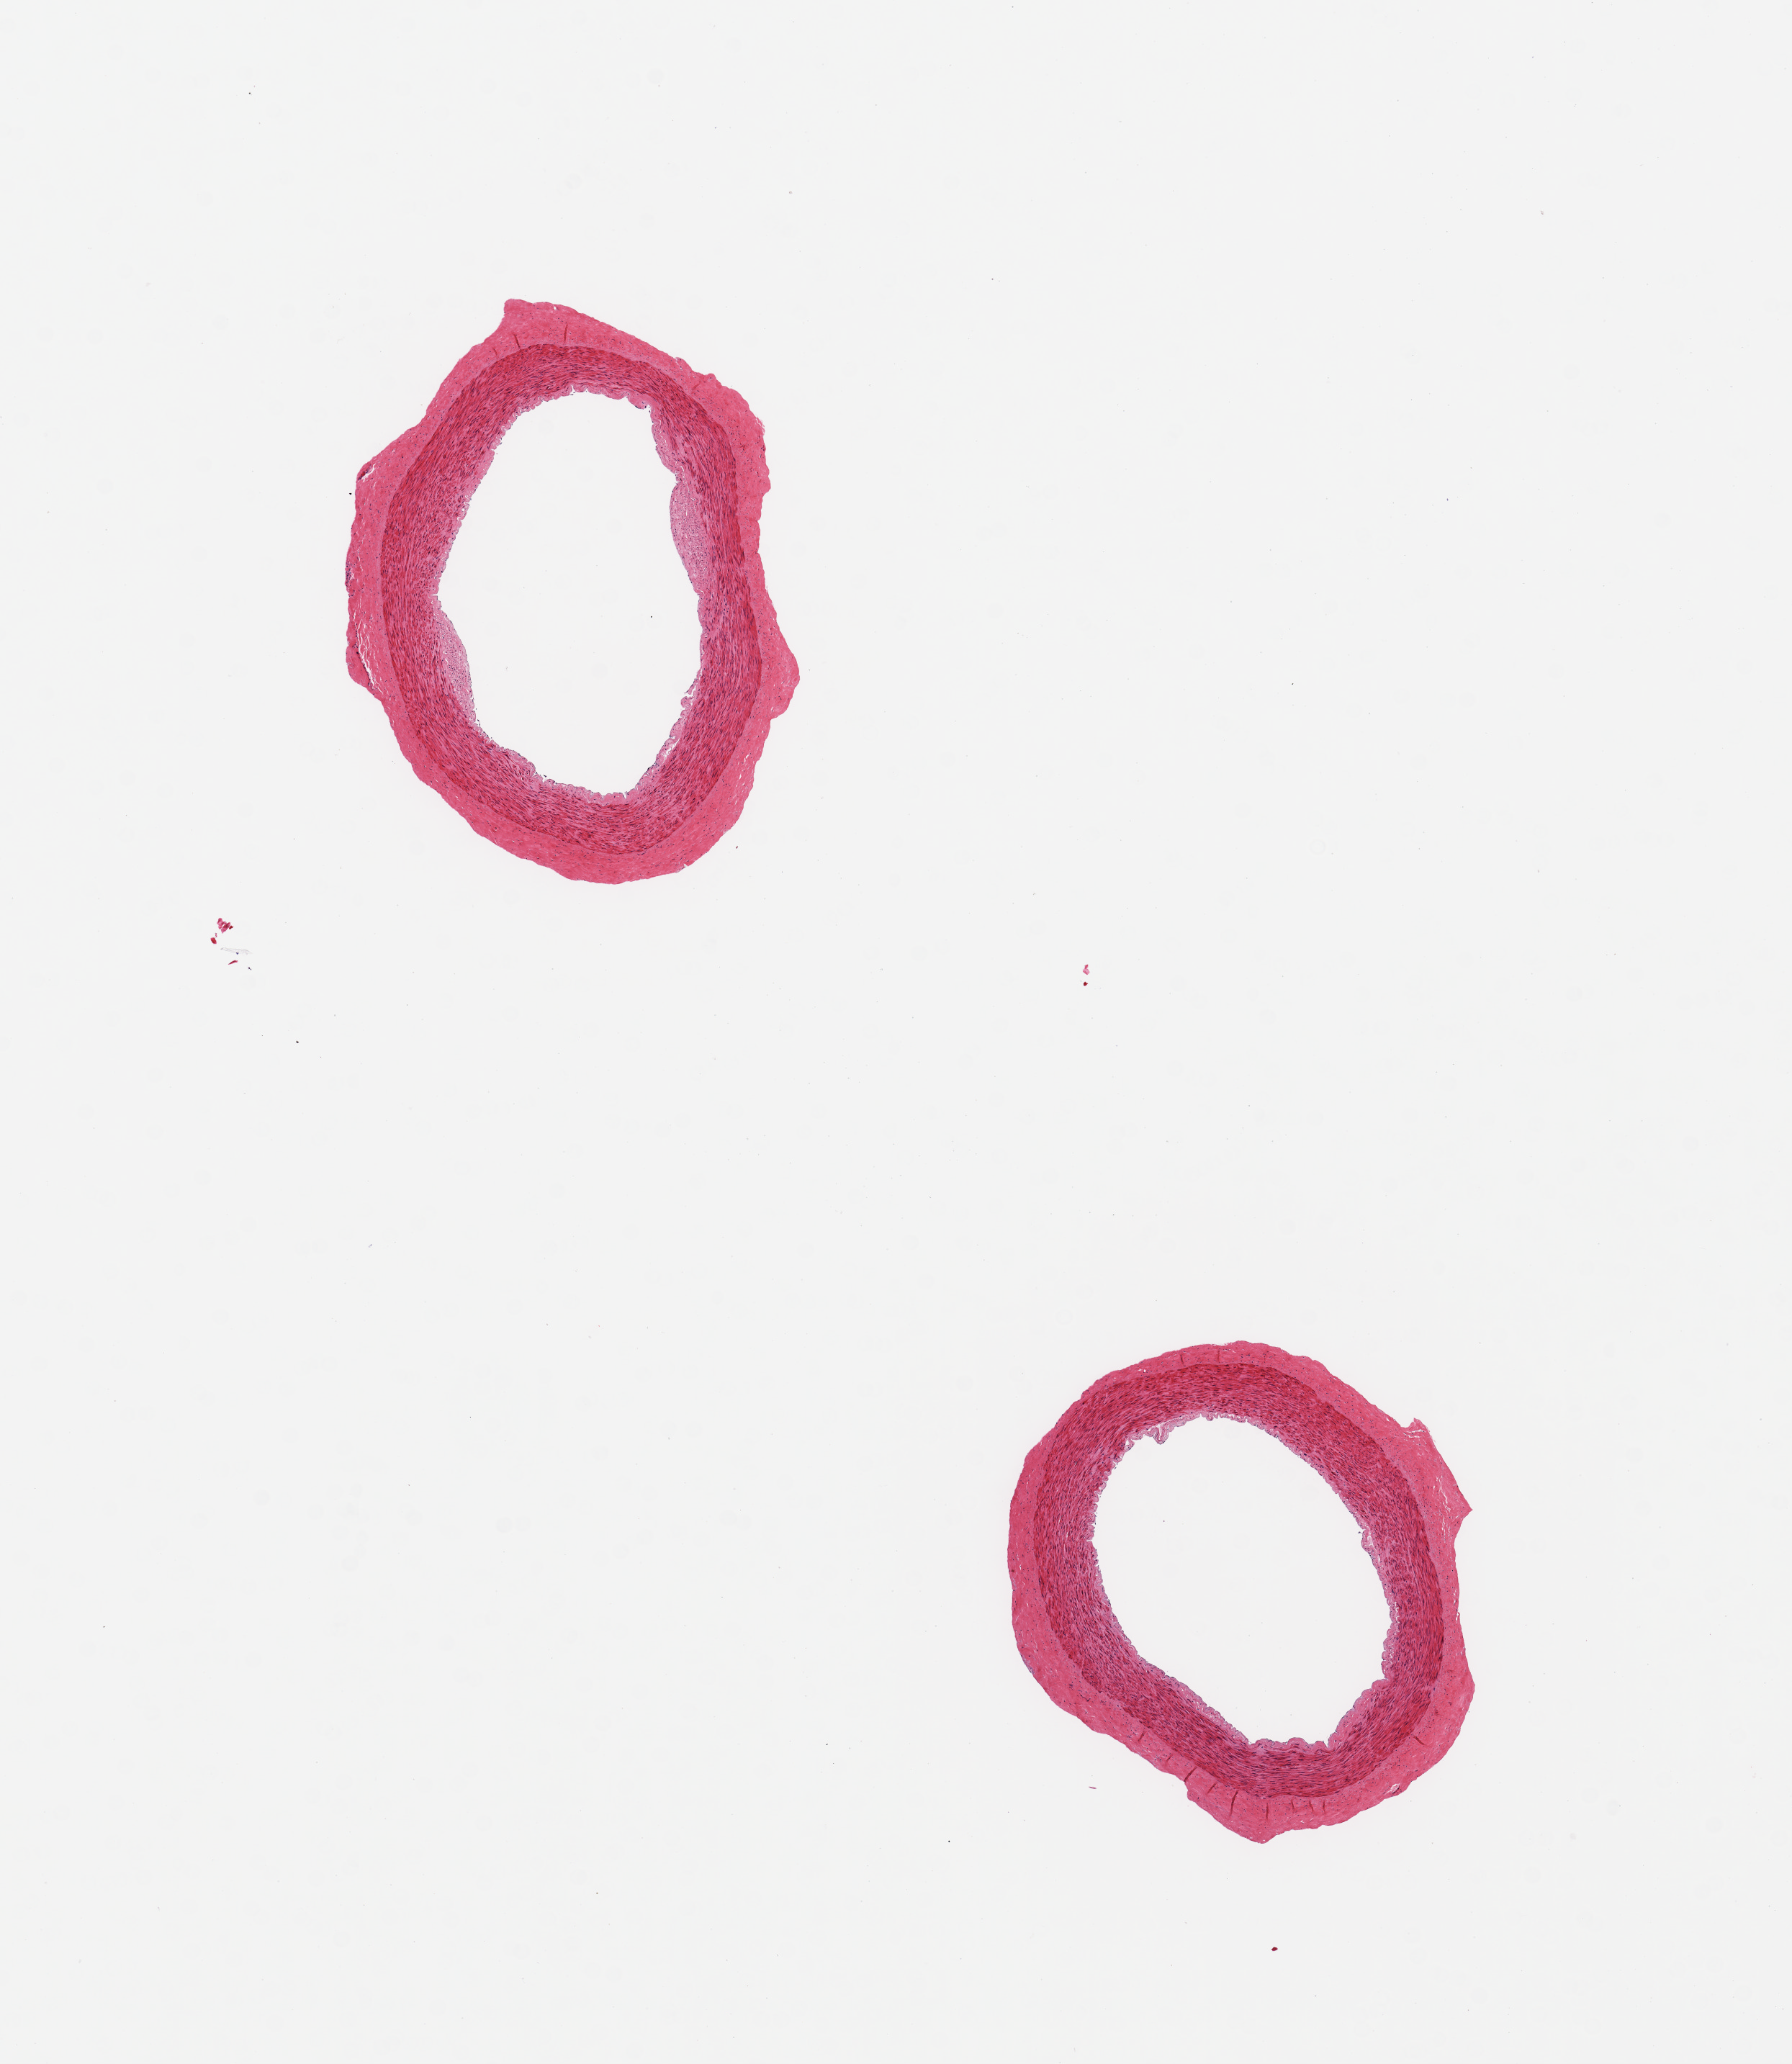
Hematoxylin and eosin (H&E) whole-slide image, shown as a low-resolution overview of the whole scanned area (about 9.8 x 11.3 mm, from a 20x scan), PAXgene-fixed, paraffin-embedded tissue, section of tibial artery (target tissue), tissue donor sample.
Pathologist's review note for this sample: 2 pieces; minimal focal intimal fibrous thickening; well dissected; no fat in adventitia.